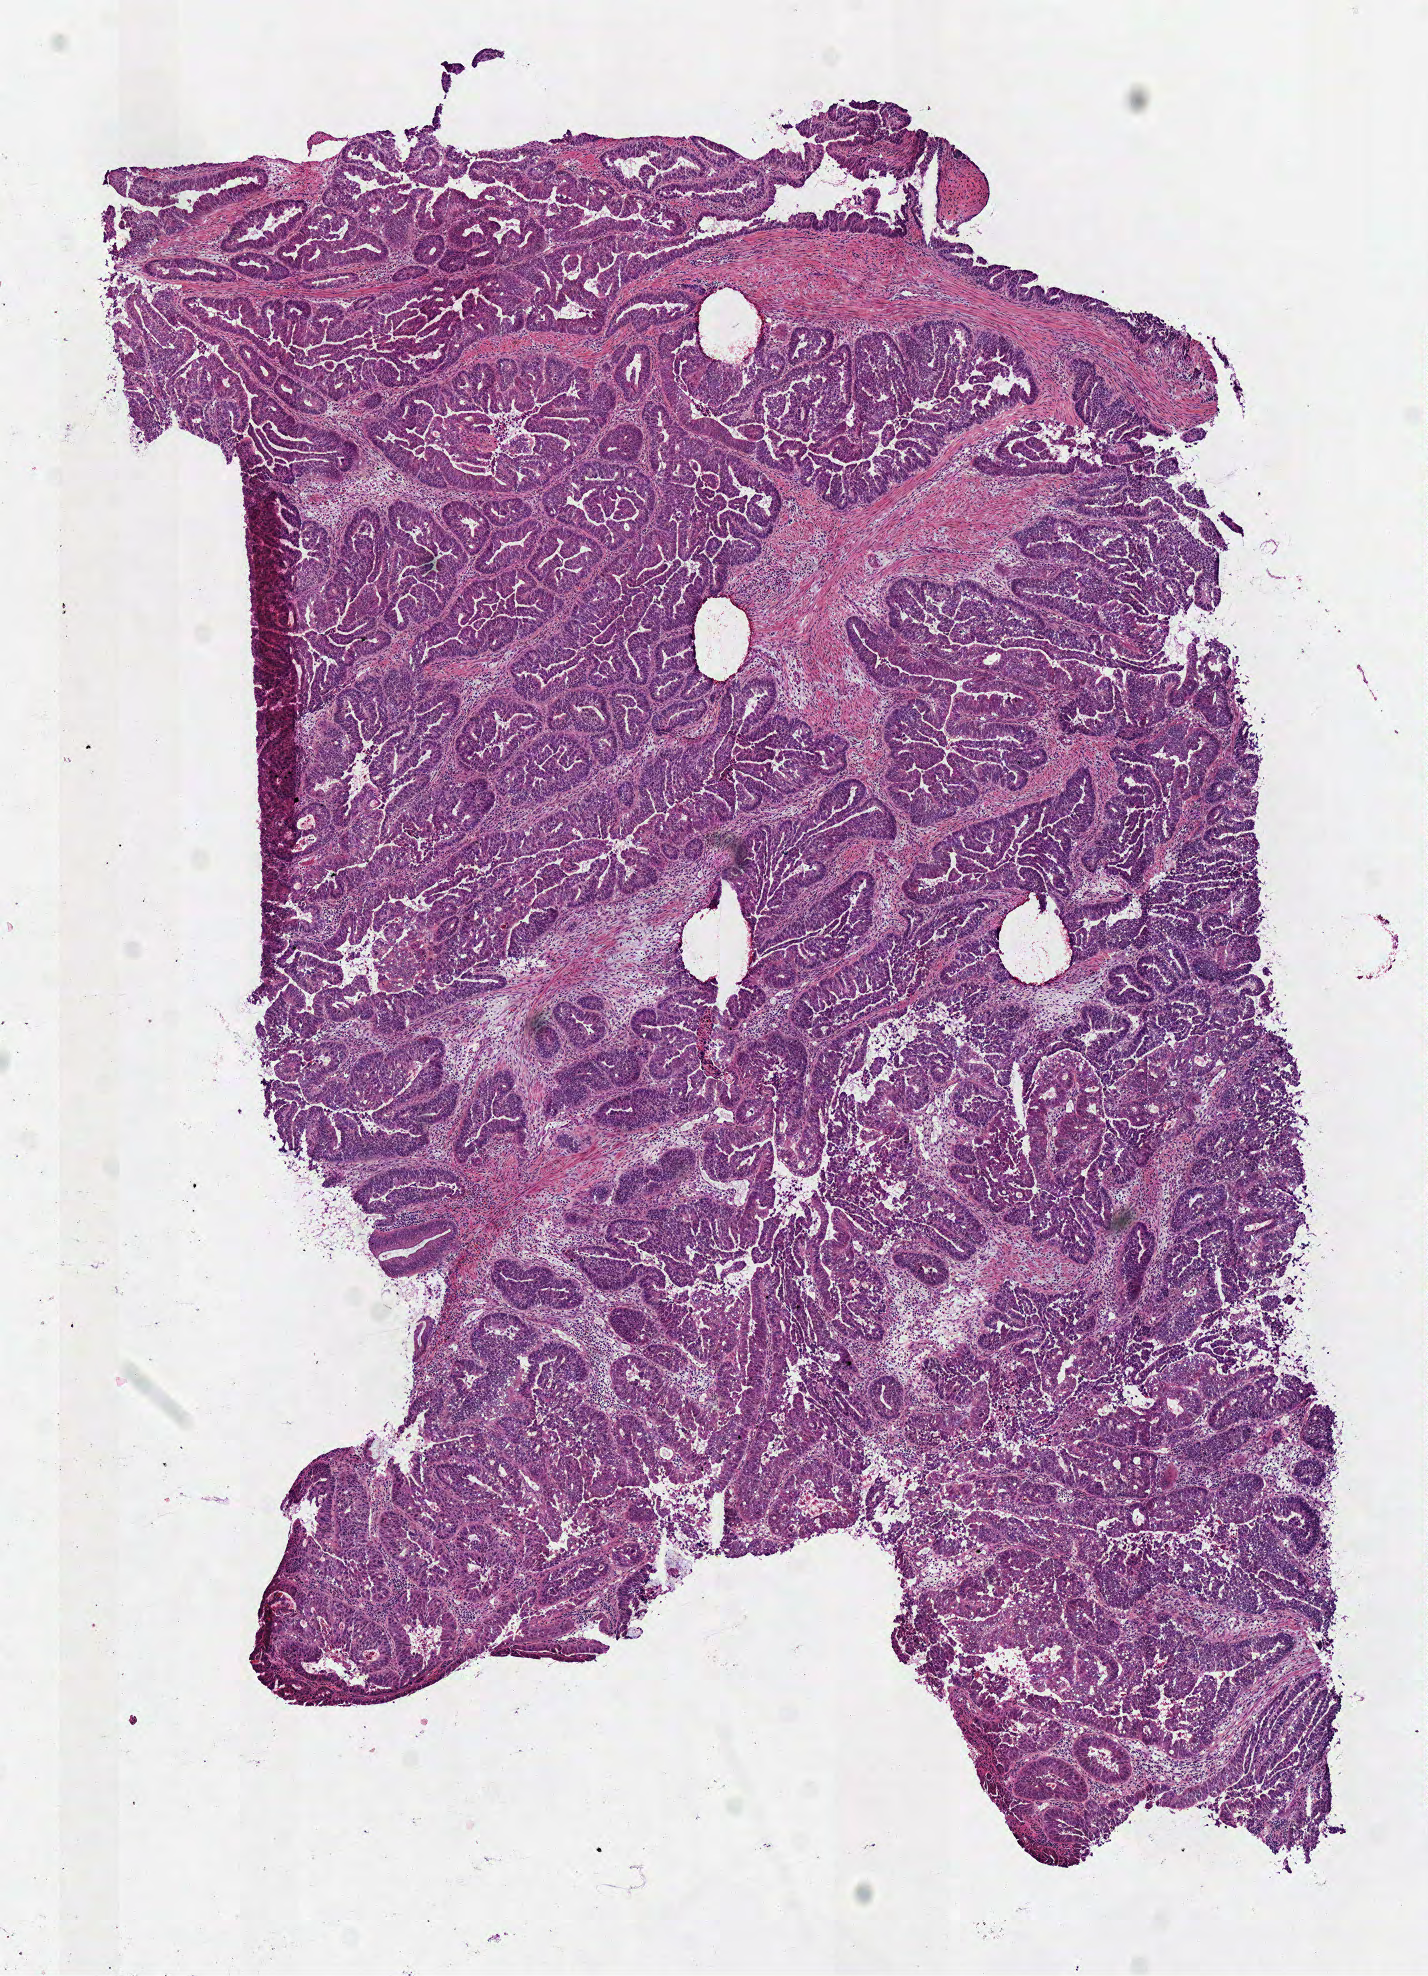
Digitized H&E-stained tissue section (whole slide), a low-resolution overview of the entire scanned area, about 5.6 x 7.8 mm (slide scanned at 40x); frozen section; rectum, primary tumour sample. Male patient; age at initial diagnosis 48 years. Composition of this section per pathologist review: tumour cells 75%, tumour nuclei 85%, normal cells 0%, stromal cells 23%, necrosis 2%. Infiltration values recorded for this section: lymphocyte infiltration 10%.
- AJCC pathologic stage: I (7th edition)
- histologic diagnosis: Adenocarcinoma, NOS (rectosigmoid junction)
- TNM: T2 N0 M0